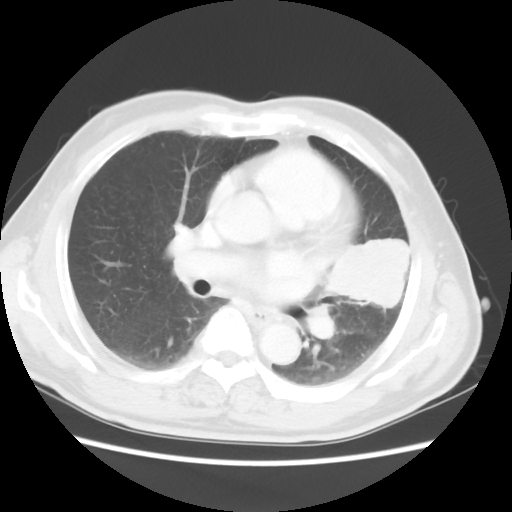
Chest CT, one axial slice; slice 27 of 50 in the series (ordered by position); reconstruction kernel STANDARD; 120 kVp; lung window (W 1500 / L -600 HU); 5 mm slice thickness; 512 × 512 image matrix, field of view 360 × 360 mm. Patient: male, 69 years. Case-level facts recorded for this patient, not image findings: clinical TNM (as recorded): T3 N1 M1a.
Annotated regions visible in this slice (bounding box drawn by a radiologist):
- lung tumour (recorded histology: squamous cell carcinoma): box from (x=322, y=227) to (x=442, y=349) px